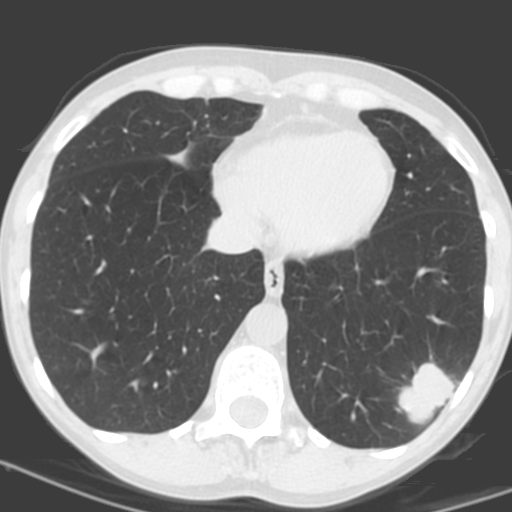
Low-dose screening chest CT, one axial slice; position 47 of 156 along the scan axis; lung window (W 1500 / L -600 HU); 512 × 512 image matrix.
Annotated regions visible in this slice (expert manual segmentation):
- lesion 1 (tumor, lower lobe of left lung): bounding box [x1, y1, x2, y2] px = [398, 363, 454, 425]